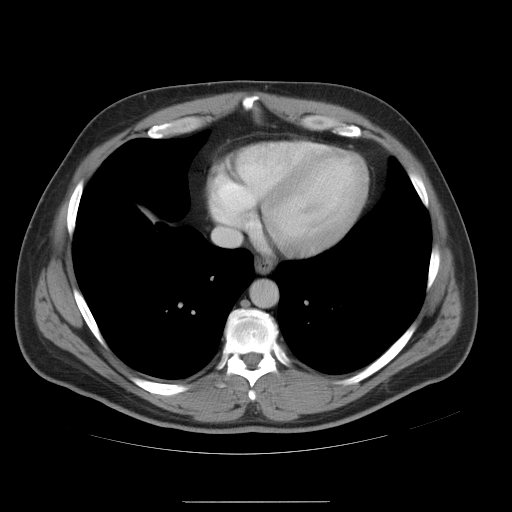
Contrast-enhanced abdominal CT, one axial slice. Slice 50 of 54 in the series (ordered by position). Soft-tissue window (W 400 / L 40 HU). 512 × 512 image matrix, field of view 436 × 436 mm. Male patient, age 40 years. From the clinical record (not read from this slice): diagnosis: colorectal cancer liver metastases, imaged before liver resection; multiple liver metastases: no; largest metastasis: 15 cm; chemotherapy before resection: no.
Structures marked on this image (manually delineated by an expert):
- hepatic veins: bounding box (x1, y1, x2, y2) in pixels: (213, 201, 261, 244)